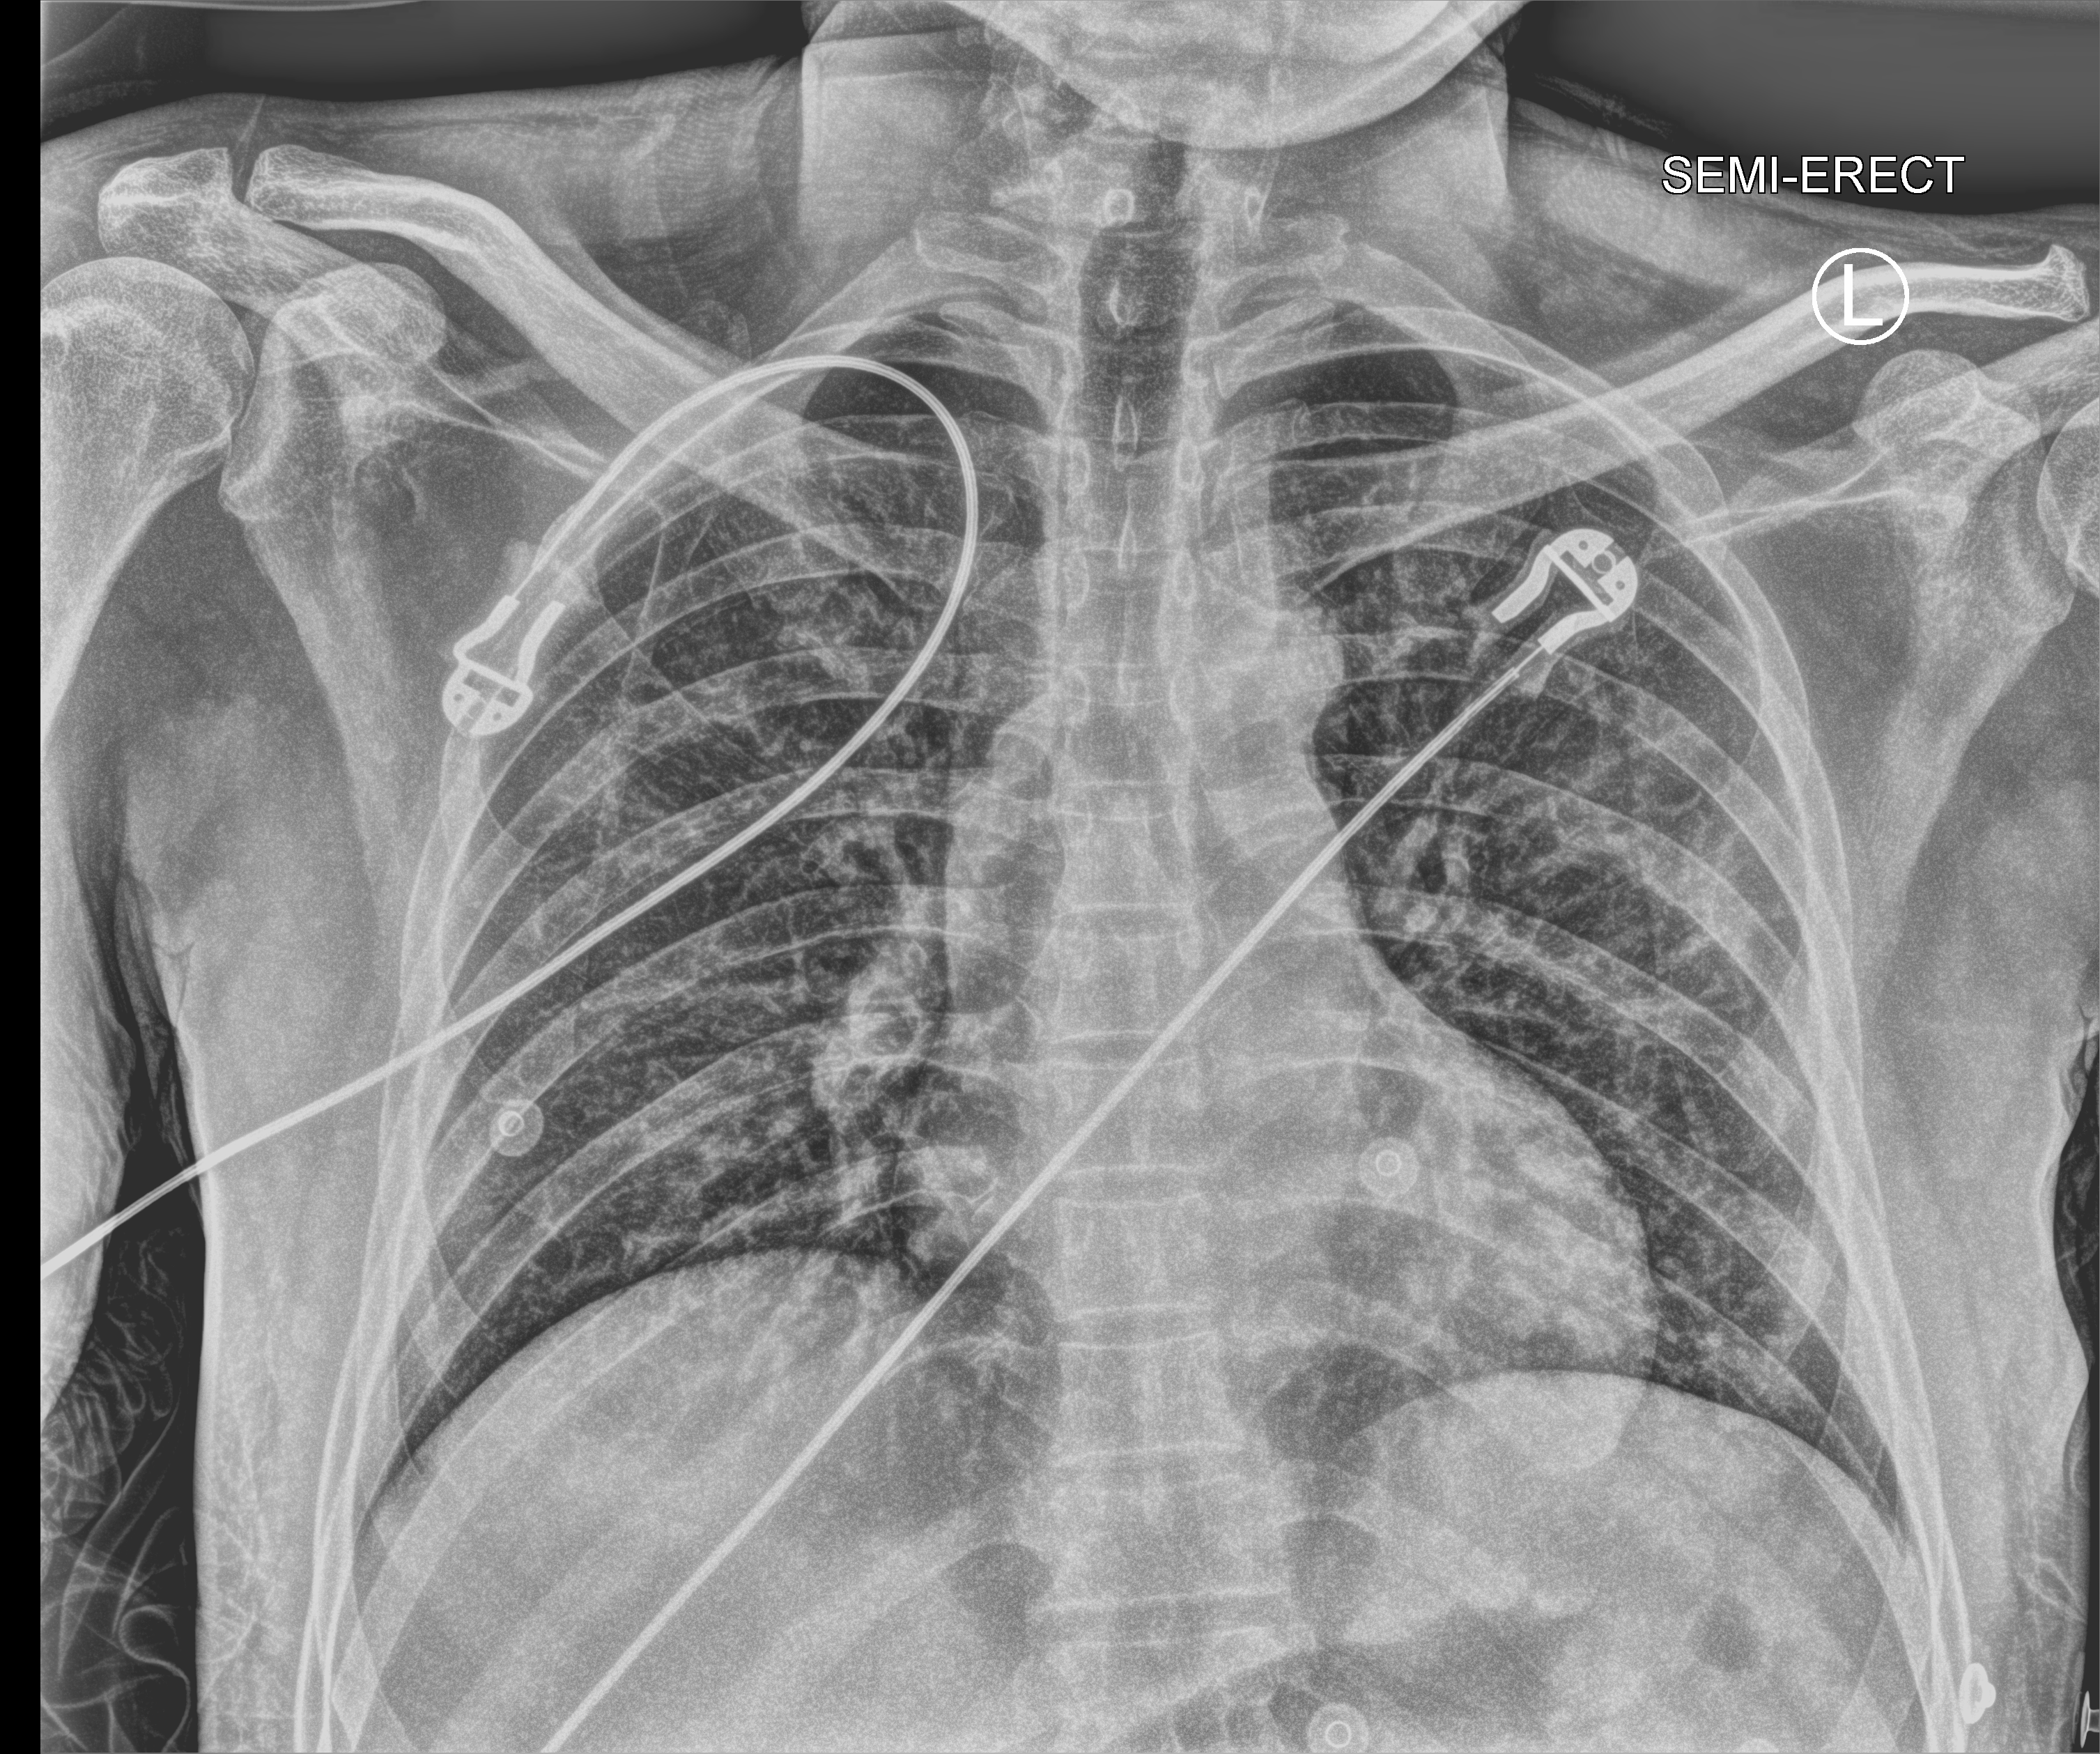
Chest X-ray (portable); anteroposterior (AP) projection. Patient hospitalised with COVID-19; male, aged 18–59 years.
Hospital-stay facts (about this admission, not read from this image; timing relative to this image not recorded): mechanically ventilated during this hospital stay: no; length of hospital stay: 4 days.